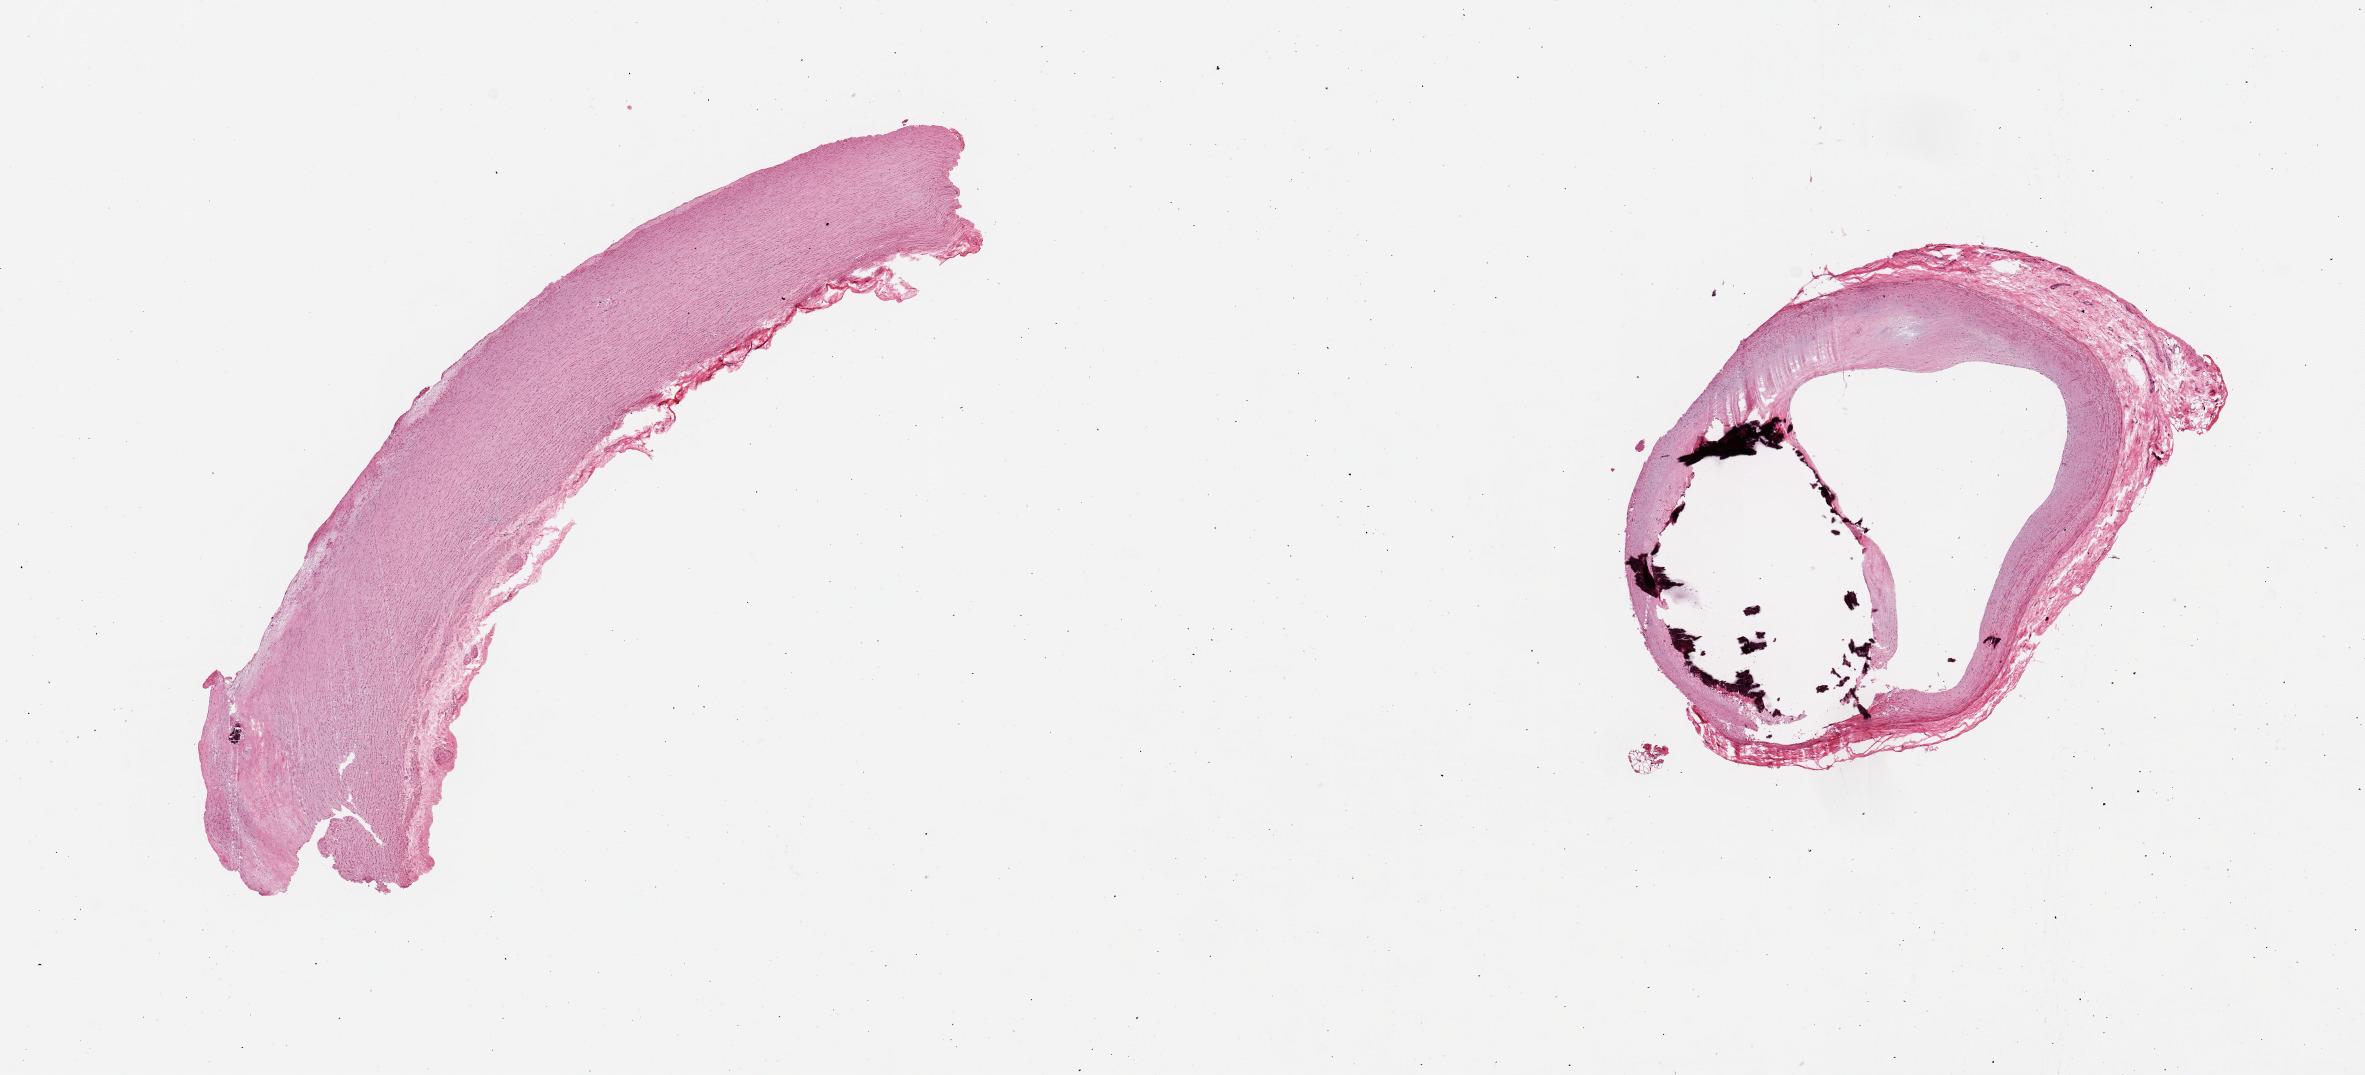
Hematoxylin and eosin (H&E) whole-slide image, a low-resolution overview of the entire scanned area, about 18.7 x 8.5 mm; PAXgene-fixed paraffin-embedded (PFPE) section; sampled site (target tissue): coronary artery; donor tissue sample. Donor sex: male.
Review note (as recorded): 2 pieces, ~60% occlusive calcifying atherosis; minimal adherent fat.